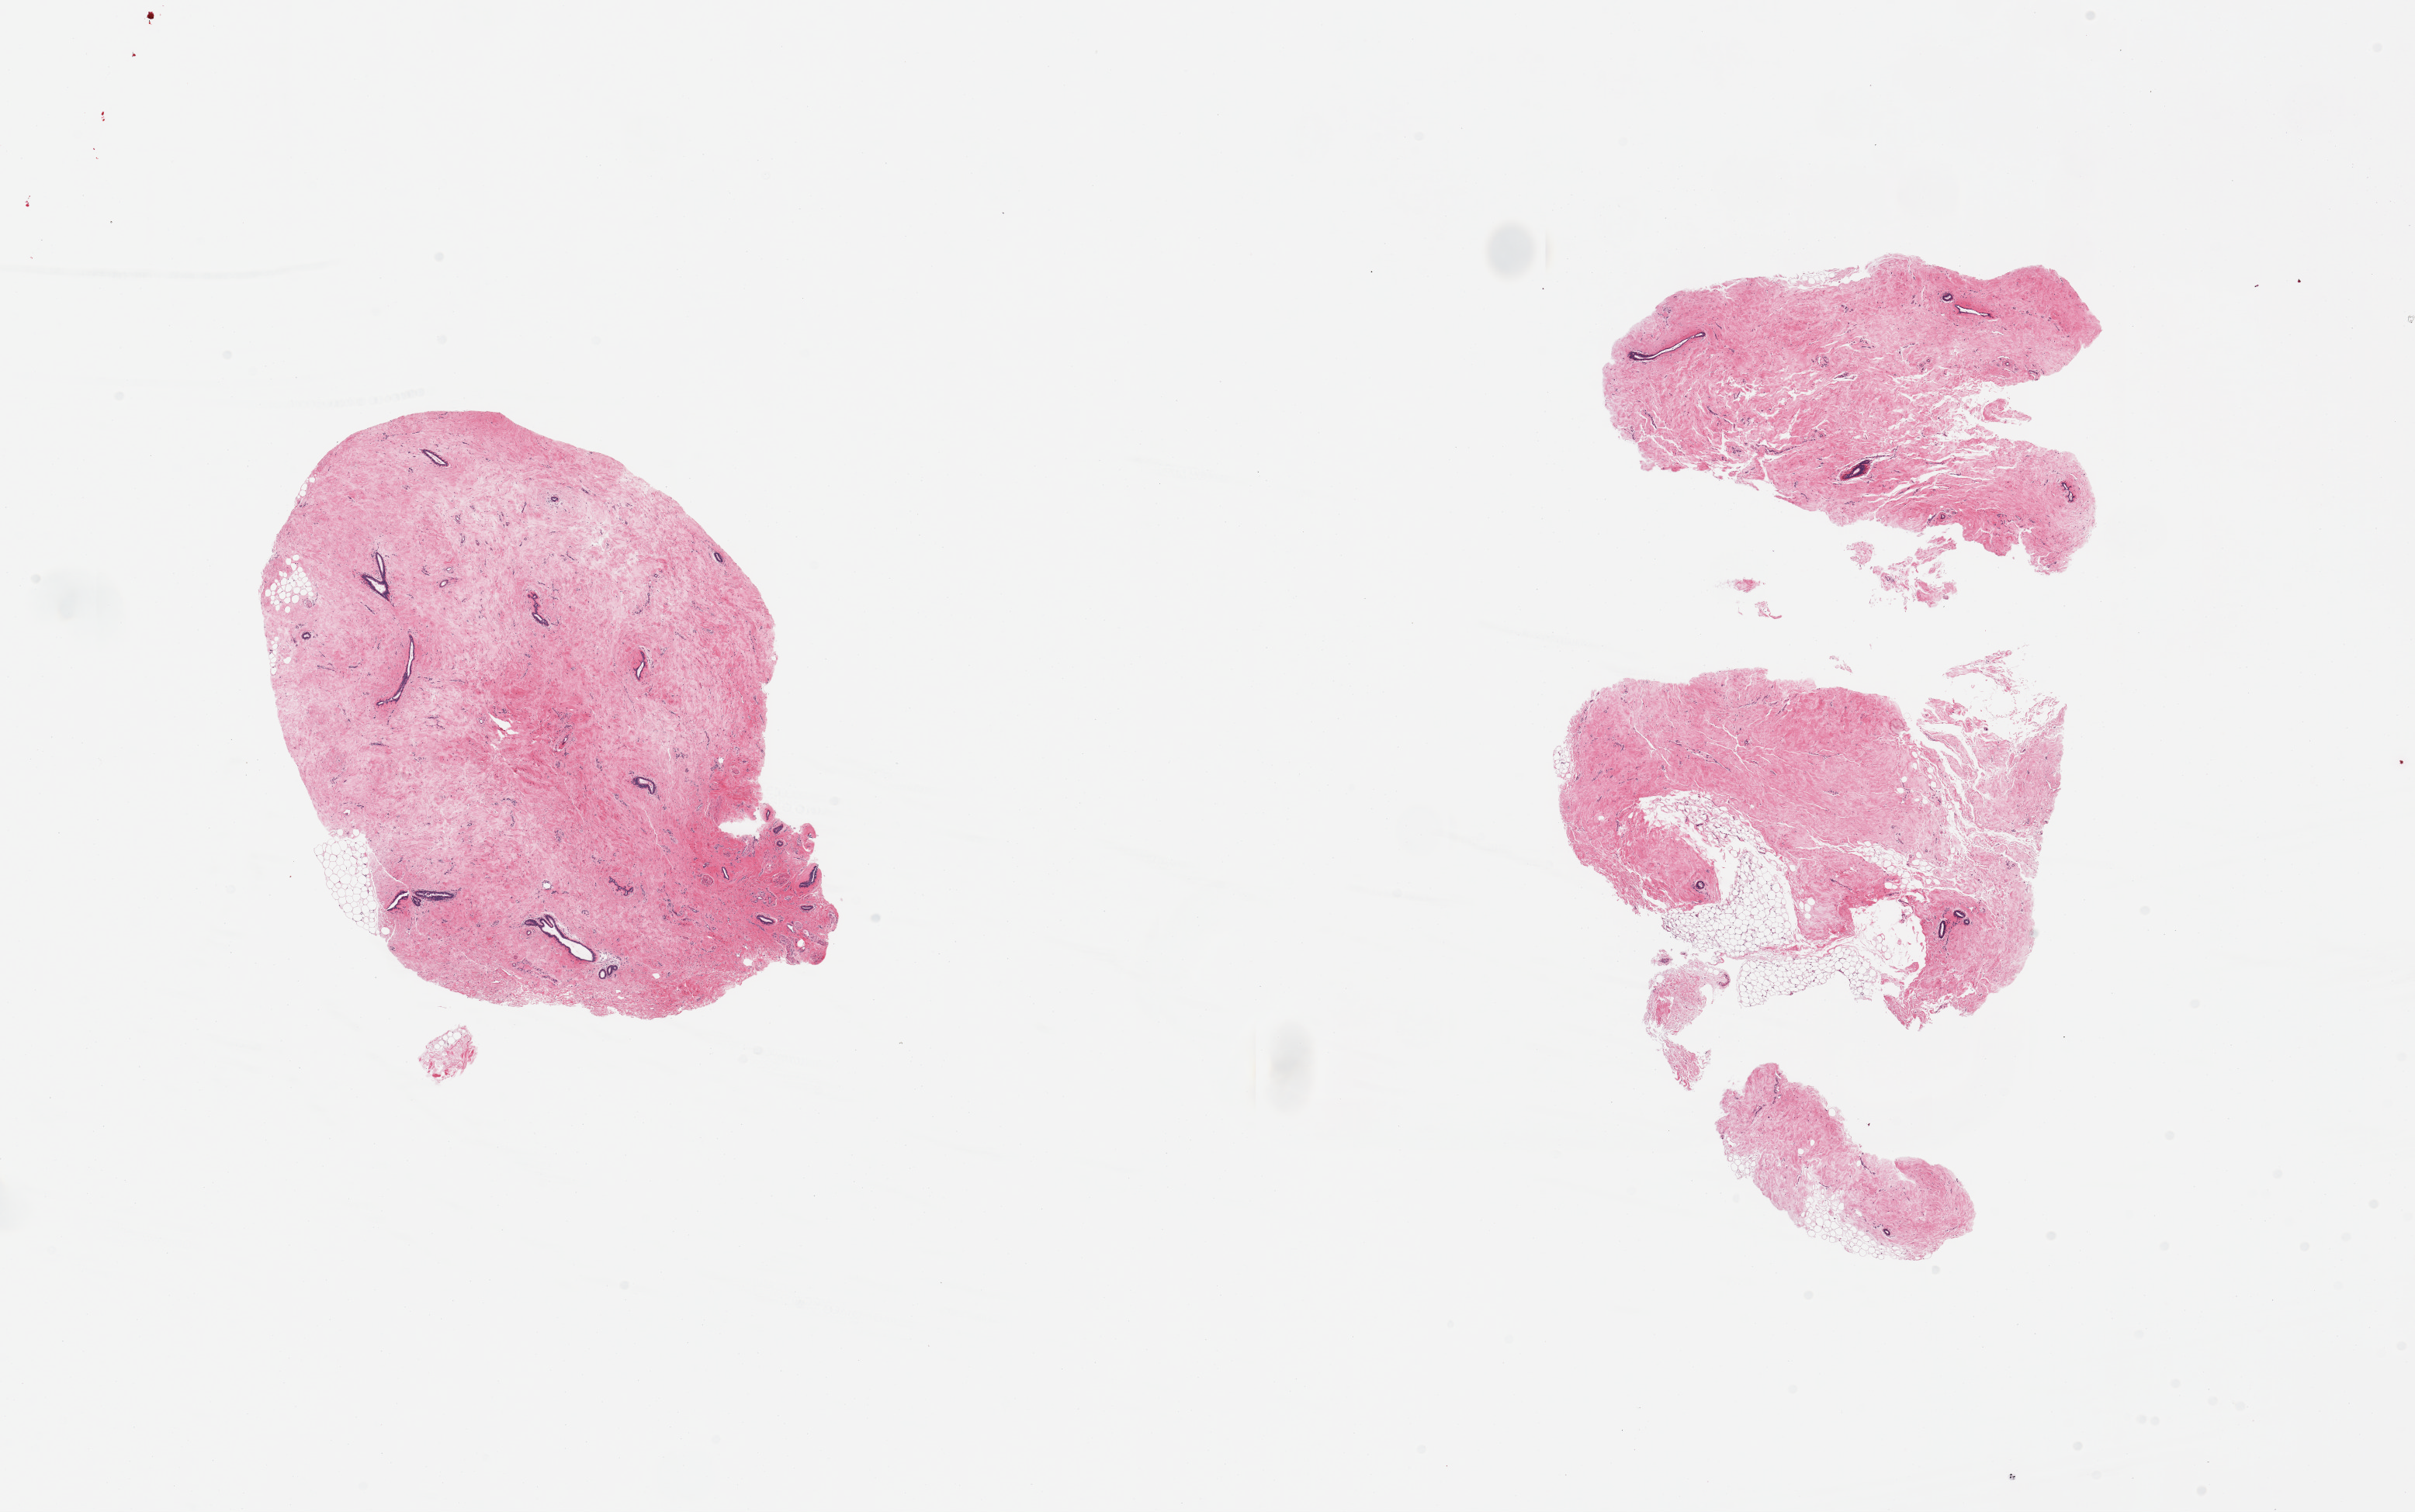
Digitized H&E-stained section — low-resolution overview of the scanned area, about 24.6 x 15.4 mm (from a 20x scan). PAXgene-fixed paraffin-embedded (PFPE) section. Sampled site (target tissue): breast. Tissue donor sample. Donor sex: male.
Pathologist's review note for this sample: 2 partially fragmented pieces; gynecomastoid changes.